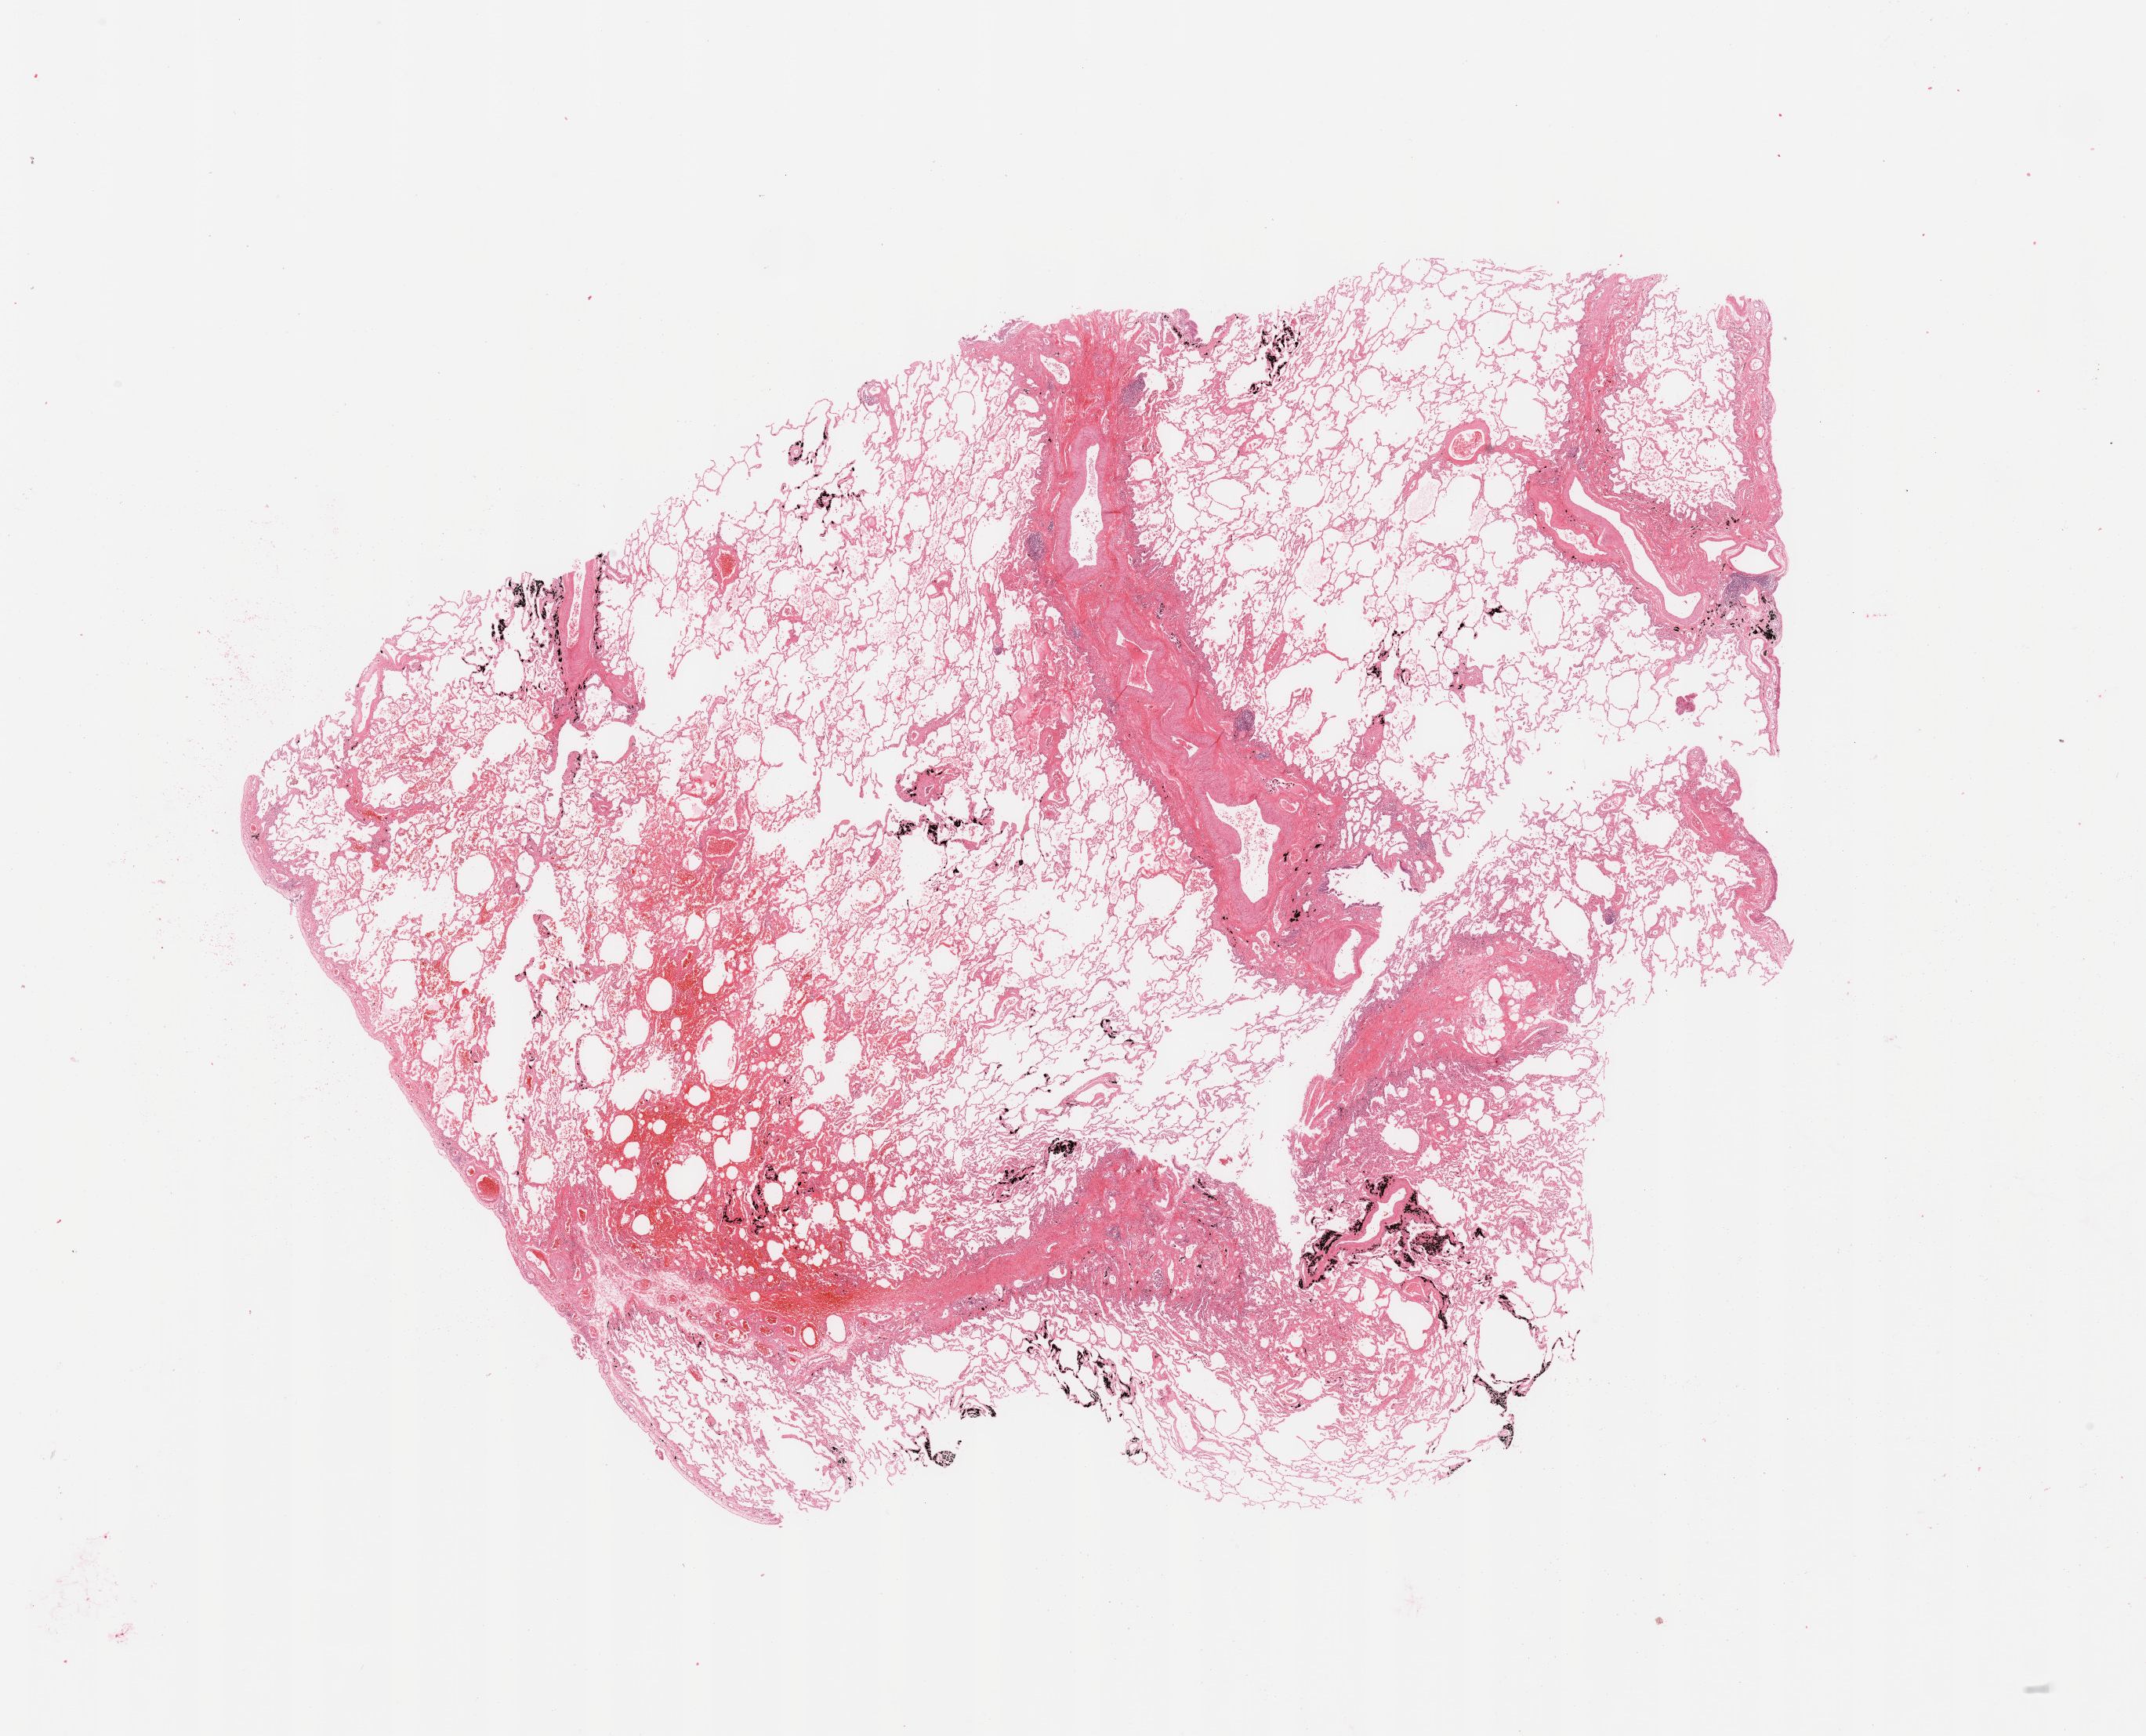
Digitized H&E tissue section (whole slide), a low-resolution overview of the entire scanned area, about 21.7 x 17.5 mm. Normal (non-tumour) tissue sample, sampled site: lung. 59-year-old male patient.
This section: normal (non-tumour) tissue from the same patient. Patient diagnosis: Adenocarcinoma, NOS.